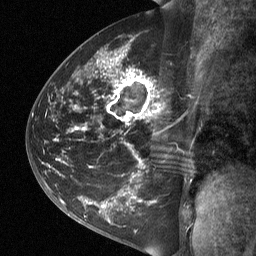
Breast MRI (dynamic contrast-enhanced), one sagittal slice; position 34 of 64 along the scan axis; dynamic contrast-enhanced study with each time point stored as its own series, time point 2 of 3 at this slice position (early post-contrast, ordered by acquisition time); 1.5 T; TE 4.8 ms, TR 27 ms; 2 mm slice thickness; 256 × 256 image matrix, field of view 200 × 200 mm. Female patient, age 42 years. Case-level facts recorded for this patient, not image findings: setting: breast cancer imaged before/during neoadjuvant chemotherapy; receptor status: triple-negative.
Structures marked on this image (semi-automatic segmentation, software-assisted and operator-edited):
- analysis volume of interest (the breast-tissue region the enhancement analysis was run in; not a lesion): bounding box (x1, y1, x2, y2) in pixels: (49, 45, 194, 197)
- tumour enhancement mask (voxels above the 90 % enhancement threshold inside the analysis volume of interest): (114, 58, 161, 118)